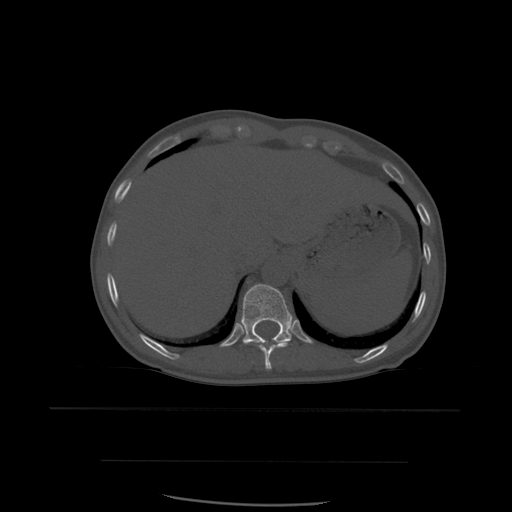
CT including the spine, one axial slice; slice 302 of 574 in the series (ordered by position); bone window (W 1800 / L 400 HU); 512 × 512 image matrix, field of view 392 × 392 mm. Patient age 48 years. From the clinical record (not read from this slice): primary cancer: lung.
Annotated regions visible in this slice (semi-automatically segmented with operator editing):
- T10 vertebra: bounding box <258,342,289,370> (left, top, right, bottom; pixels)
- T11 vertebra: <241,284,293,346>